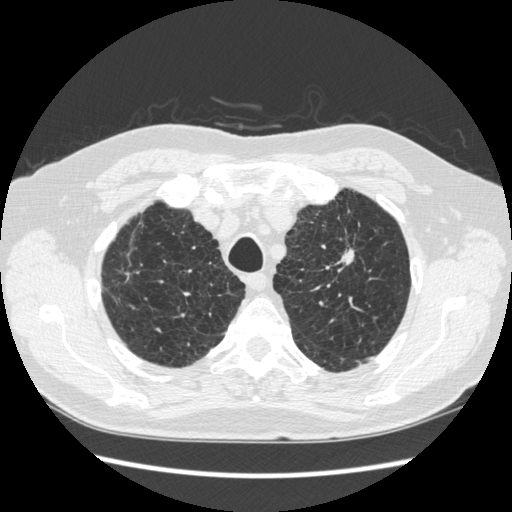
Low-dose screening chest CT, one axial slice; reconstruction kernel STANDARD; lung window (W 1500 / L -600 HU); 1.25 mm slice thickness; 512 × 512 image matrix, field of view 360 × 360 mm.
Outlined on this slice (expert manual segmentation):
- lesion 1 (tumor, upper lobe of left lung): box from (x=339, y=249) to (x=354, y=265) px